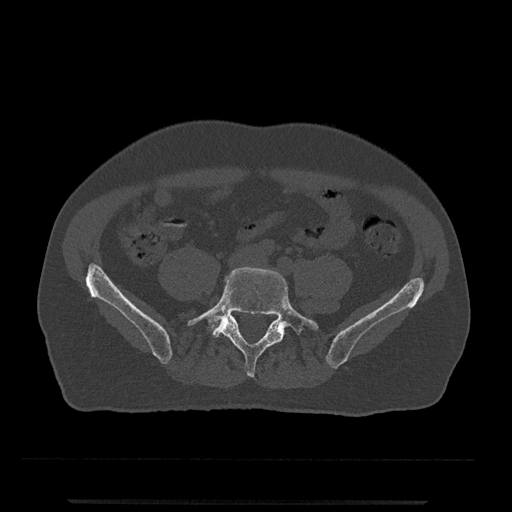
CT including the spine, one axial slice. Position 74 of 797 along the scan axis. Reconstruction kernel Br40s/3. 120 kVp. Bone window (W 1800 / L 400 HU). 0.5 mm slice thickness. 512 × 512 image matrix, field of view 419 × 419 mm. Patient: male, 63 years. Case-level facts recorded for this patient, not image findings: primary cancer: prostate.
Annotated regions visible in this slice (semi-automatic segmentation, software-assisted and operator-edited):
- L5 vertebra: box from (x=187, y=267) to (x=319, y=378) px